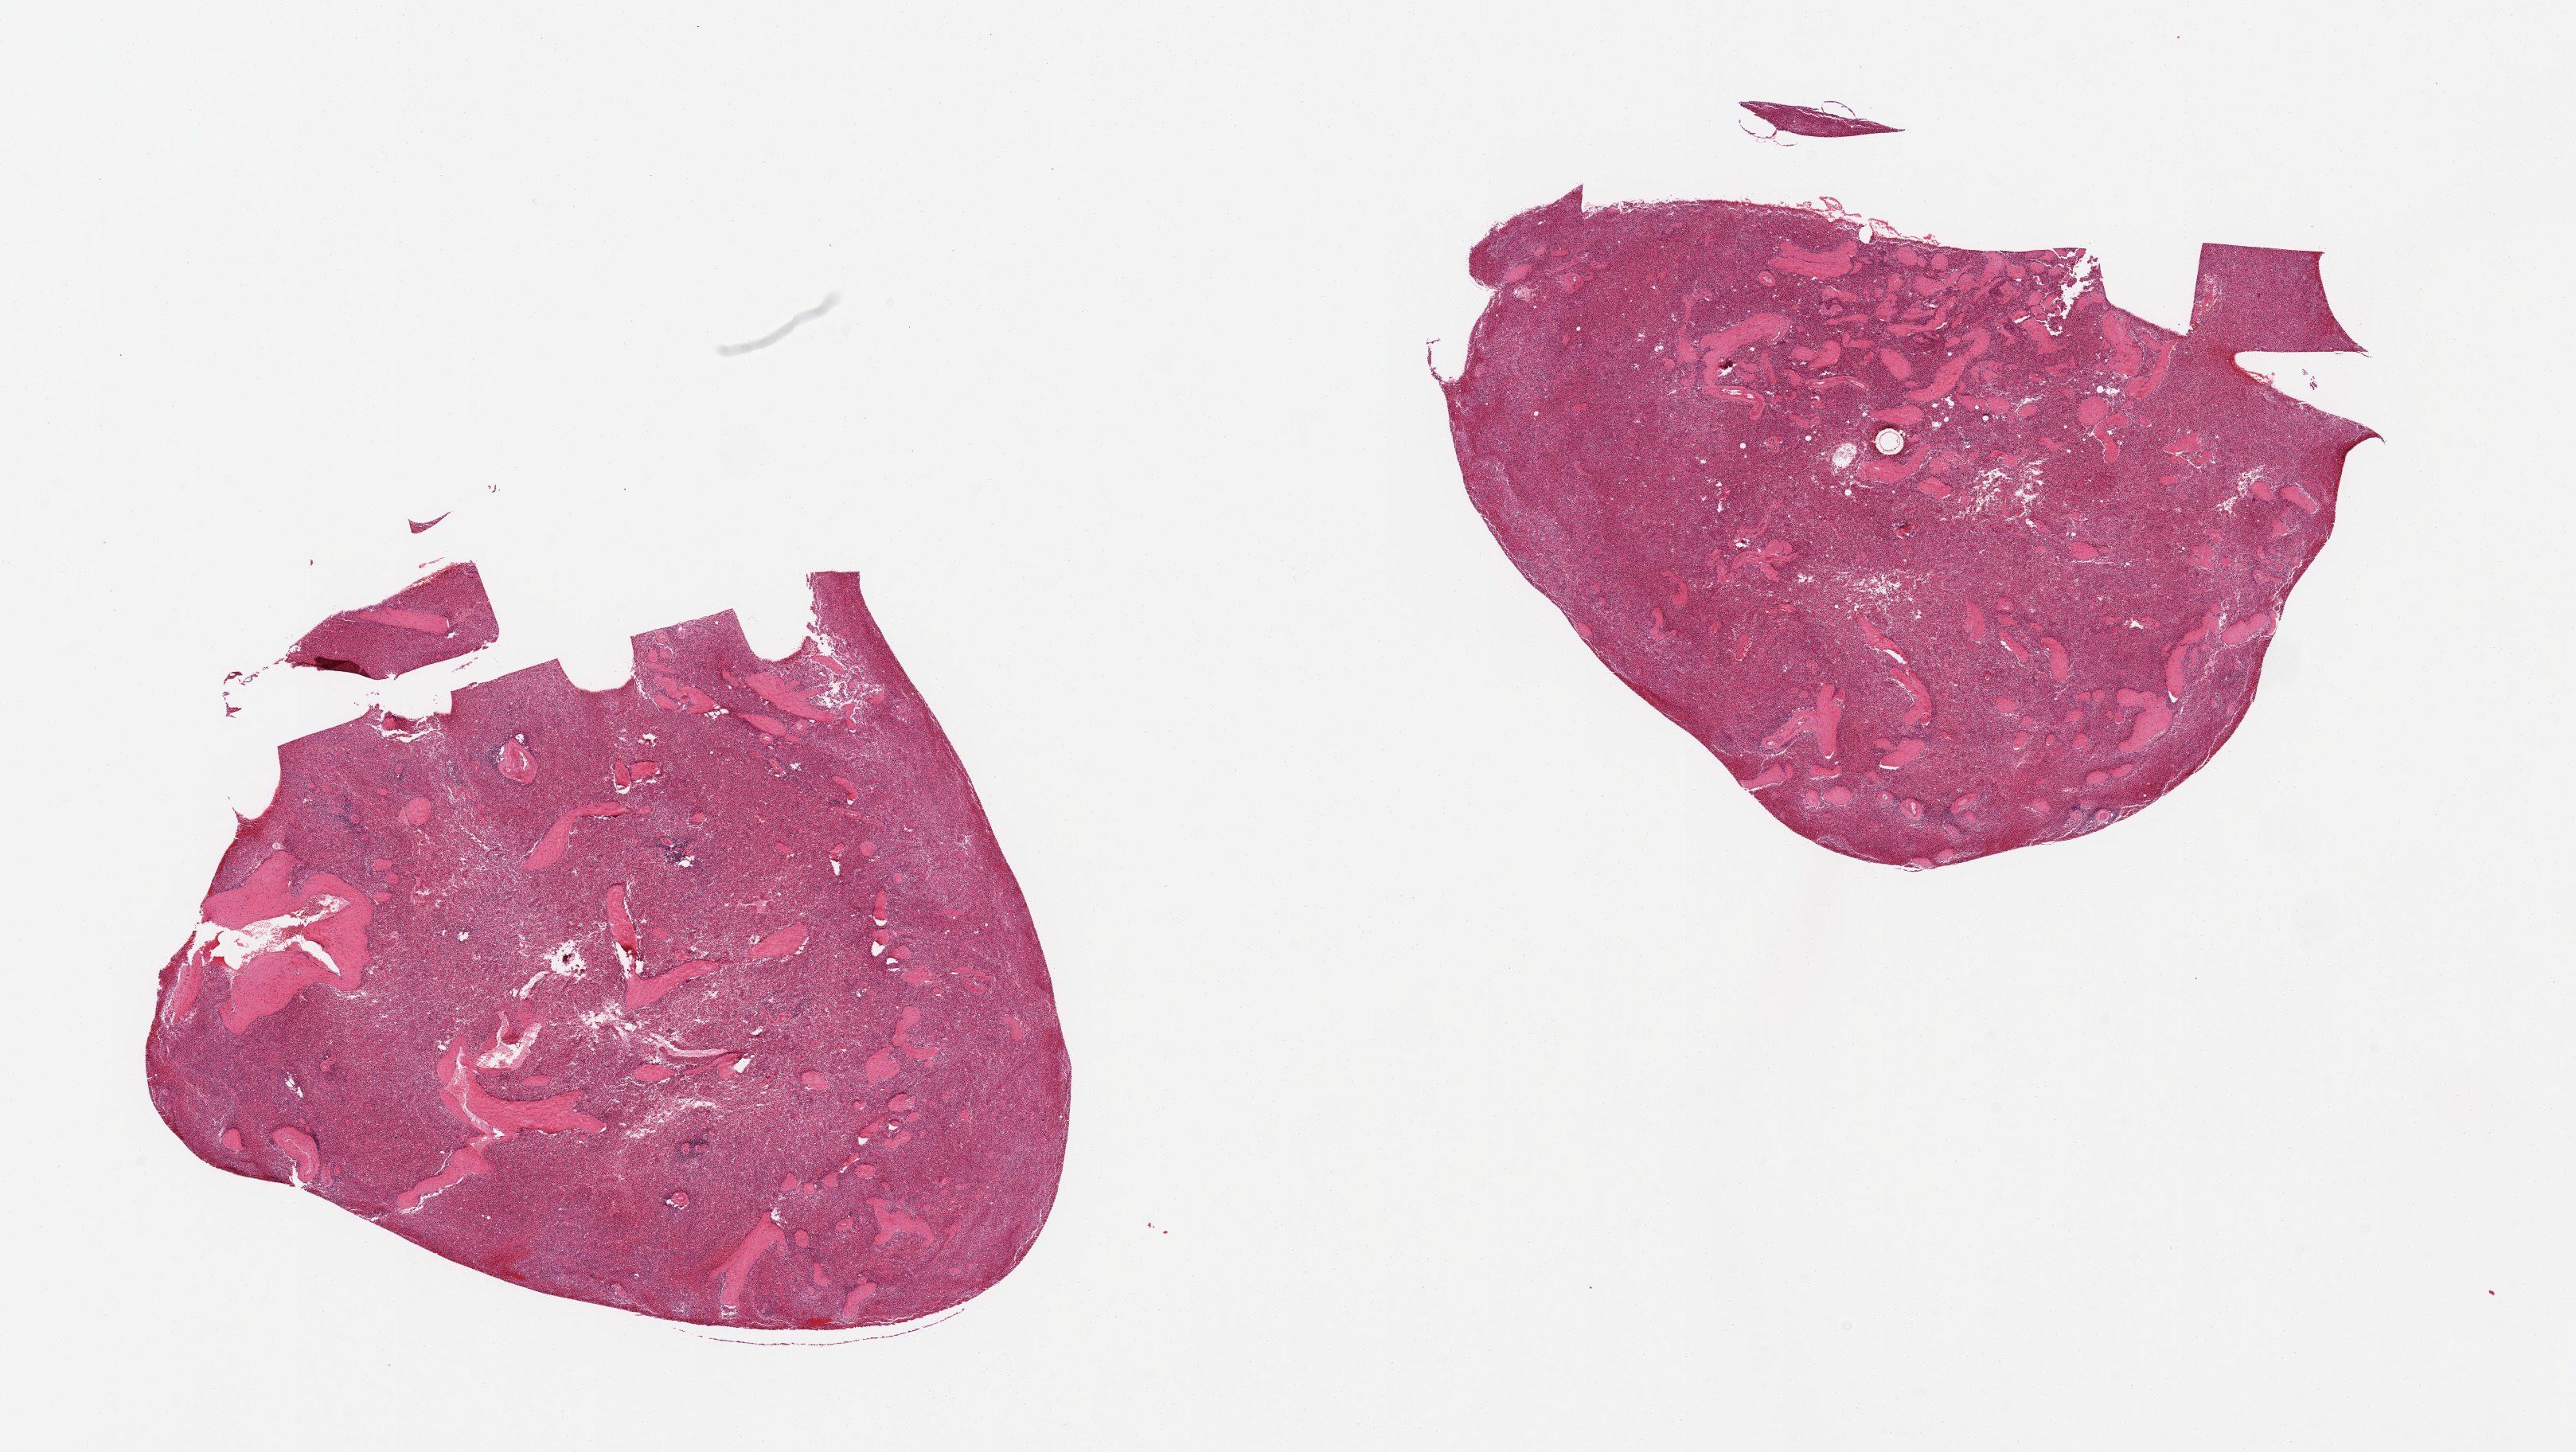
Hematoxylin and eosin (H&E) whole-slide image — whole scanned area (about 25.6 x 14.4 mm) shown as a low-resolution overview. PAXgene-fixed paraffin-embedded (PFPE) section. Section of spleen (target tissue). Donor tissue sample.
• reviewer comment on this tissue sample: 2 pieces, congested red pulp, depletion of white pulp